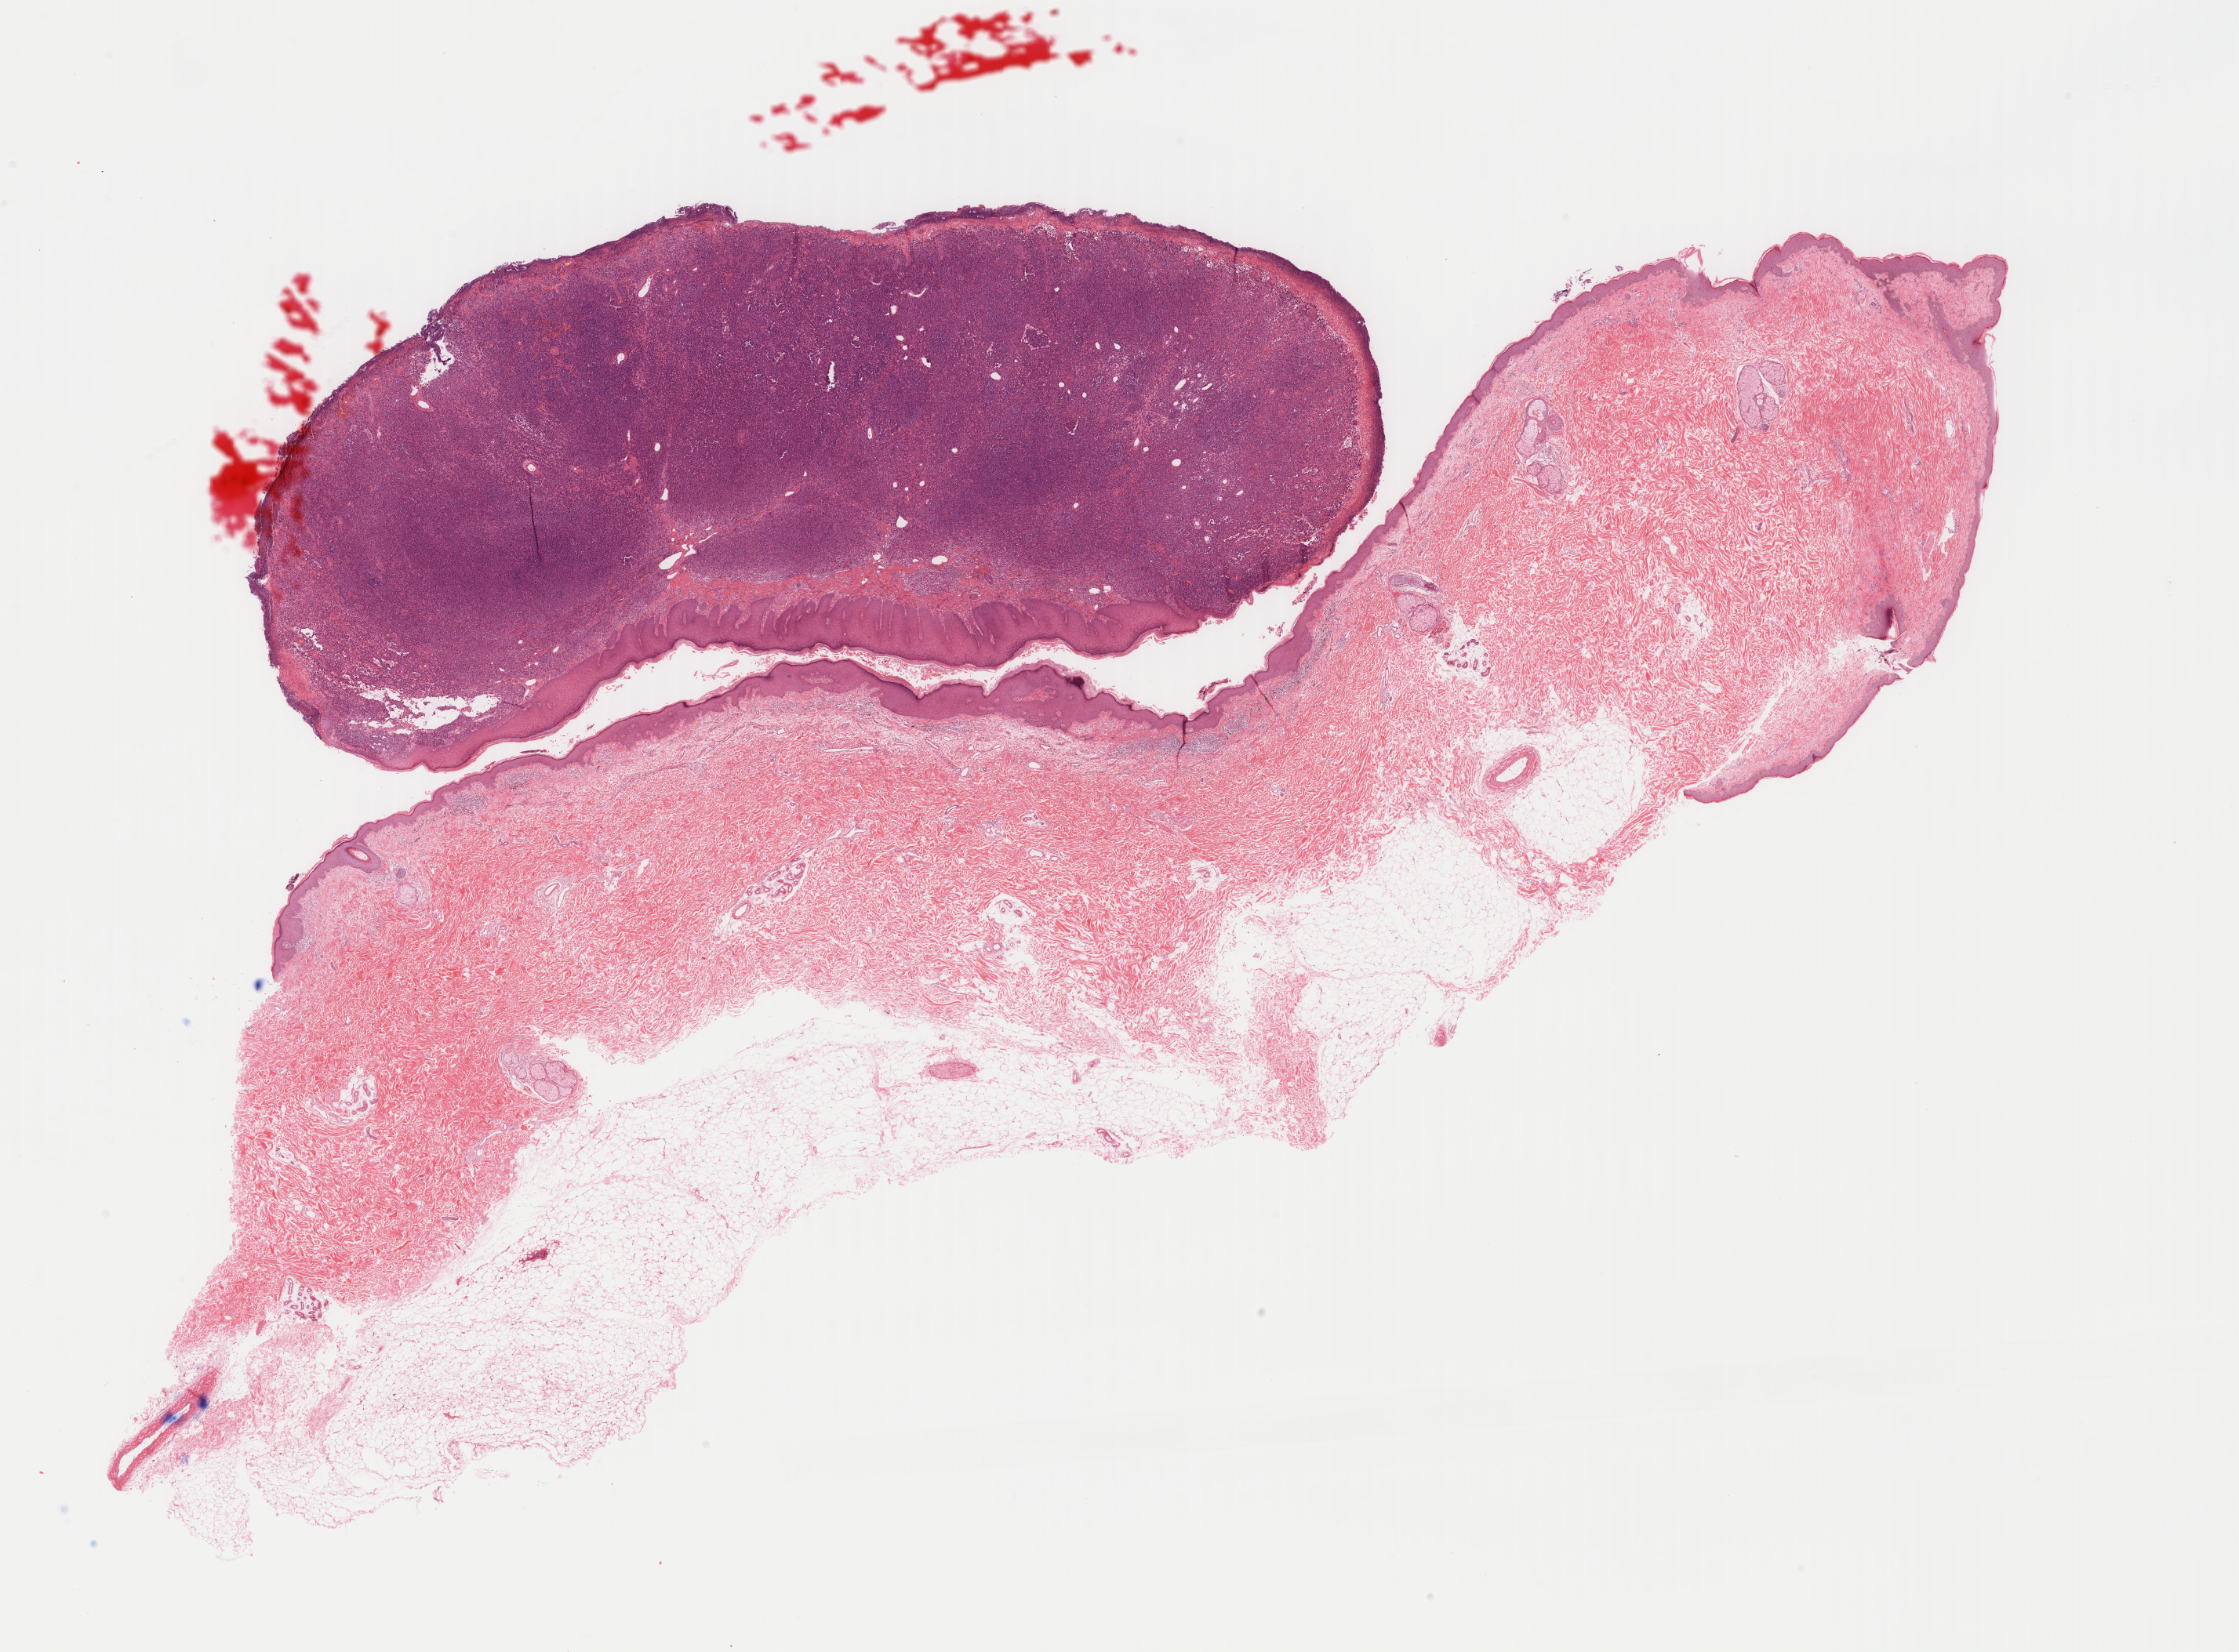
Digitized H&E-stained tissue section (whole slide) — whole scanned area (about 22.7 x 16.7 mm, acquisition: 40x scan) shown as a low-resolution overview; FFPE section; primary tumour sample from the skin. Male, age 82 years at initial diagnosis.
AJCC pathologic stage: IIC (7th edition). Diagnosis: Amelanotic melanoma. TNM: T4b N0 M0.